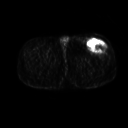
FDG PET of an extremity soft-tissue mass (from a PET/CT study), one axial slice. Slice 246 of 267 in the series (ordered by position). 128 × 128 image matrix, field of view 500 × 500 mm. Patient: male, 64 years. From the clinical record (not read from this slice): histological type: extraskeletal osteosarcoma; grade: high; site of the primary tumour: thigh.
Annotated regions visible in this slice (expert contour drawn on MRI and transferred to this co-registered scan by the dataset authors):
- gross tumour volume (mass): box from (x=88, y=40) to (x=107, y=53) px